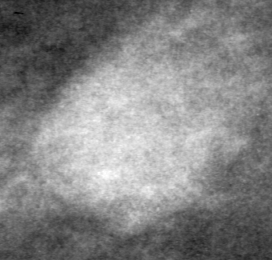
Region of interest cut from a scanned film mammogram (one marked finding); left breast; CC view; BI-RADS breast density category 2 (scale 1–4).
- Finding: mass, shape lobulated, margins obscured; BI-RADS assessment category 4; pathology (as recorded): benign.